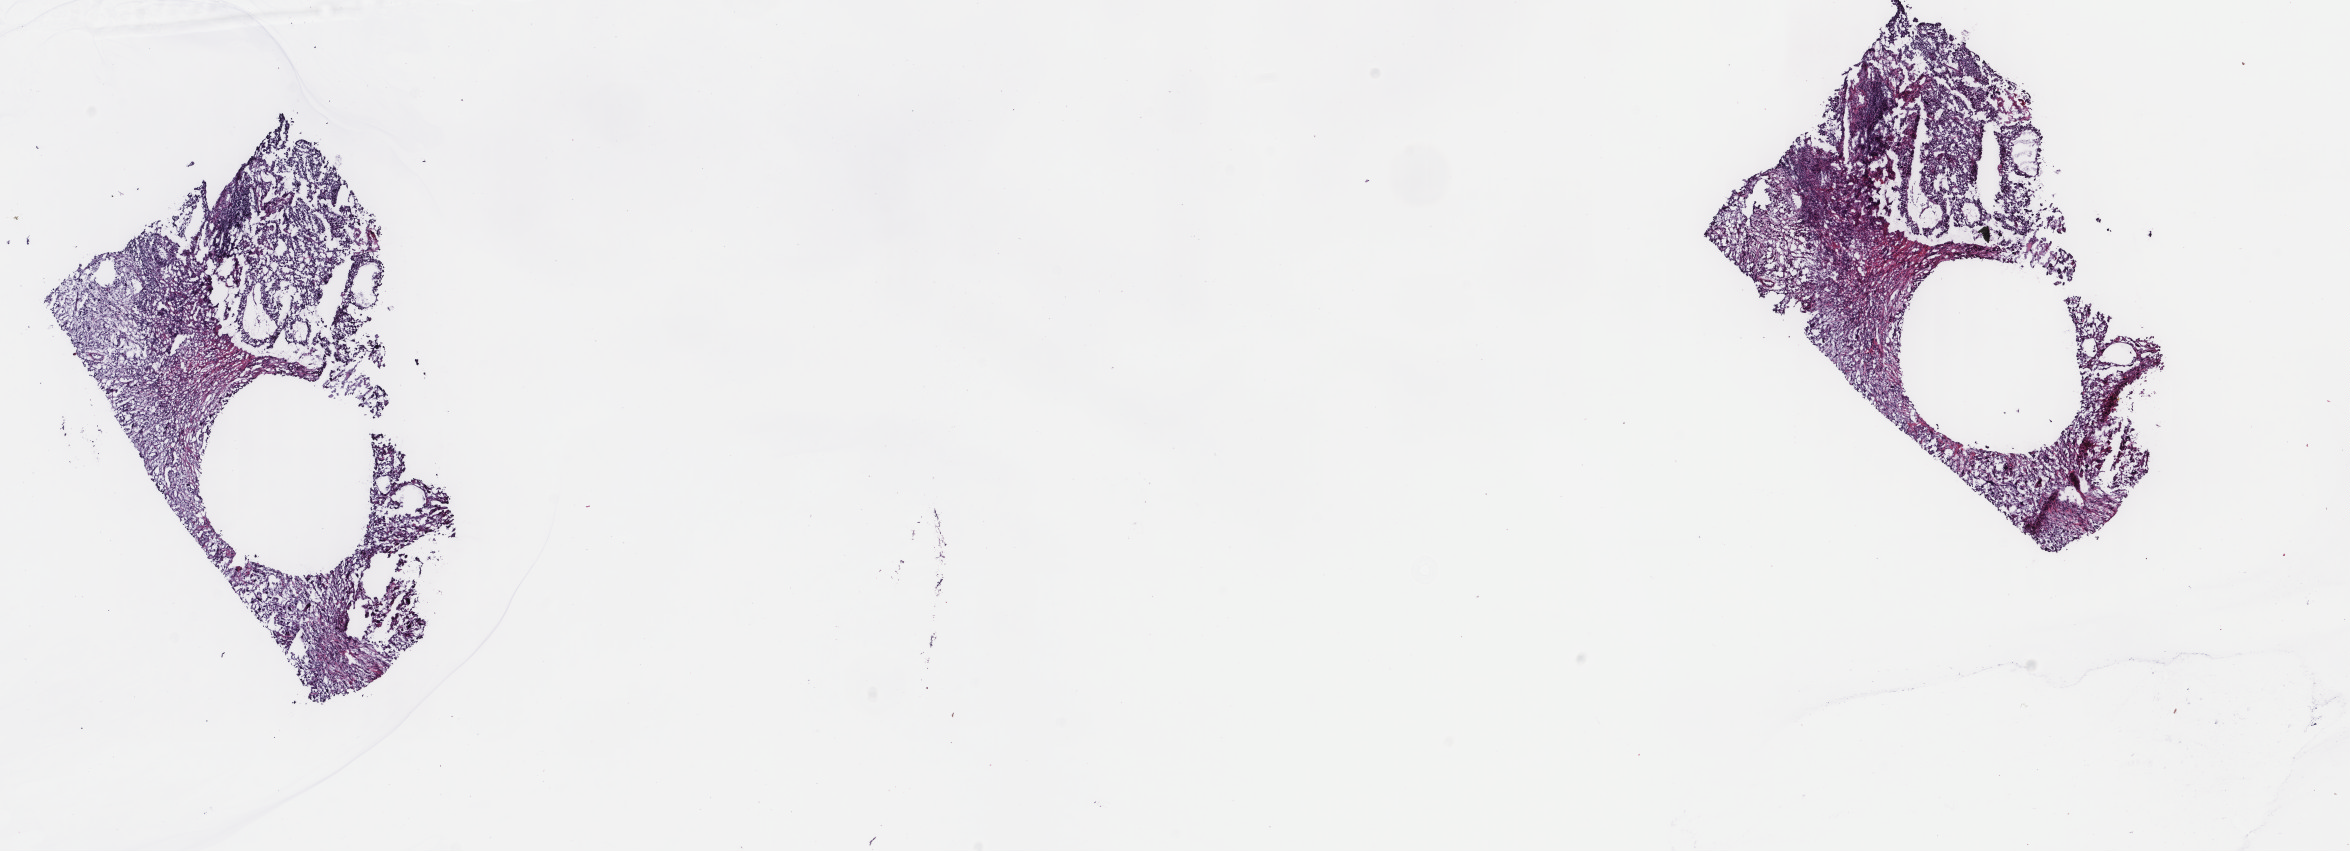
Digitized H&E tissue section (whole slide) — a low-resolution overview of the entire scanned area, about 18.7 x 6.8 mm (slide scanned at 40x); frozen section; bladder, primary tumour sample. Patient: female, age at initial diagnosis 75 years. Histologic grade: high grade. Composition of this section per pathologist review: tumour cells 65%, tumour nuclei 65%, normal cells 0%, stromal cells 35%, necrosis 0%. Inflammatory infiltration, as recorded: lymphocyte infiltration 15%, monocyte infiltration 0%, neutrophil infiltration 0%.
AJCC pathologic stage: III (6th edition). Pathologic diagnosis: Squamous cell carcinoma, NOS.